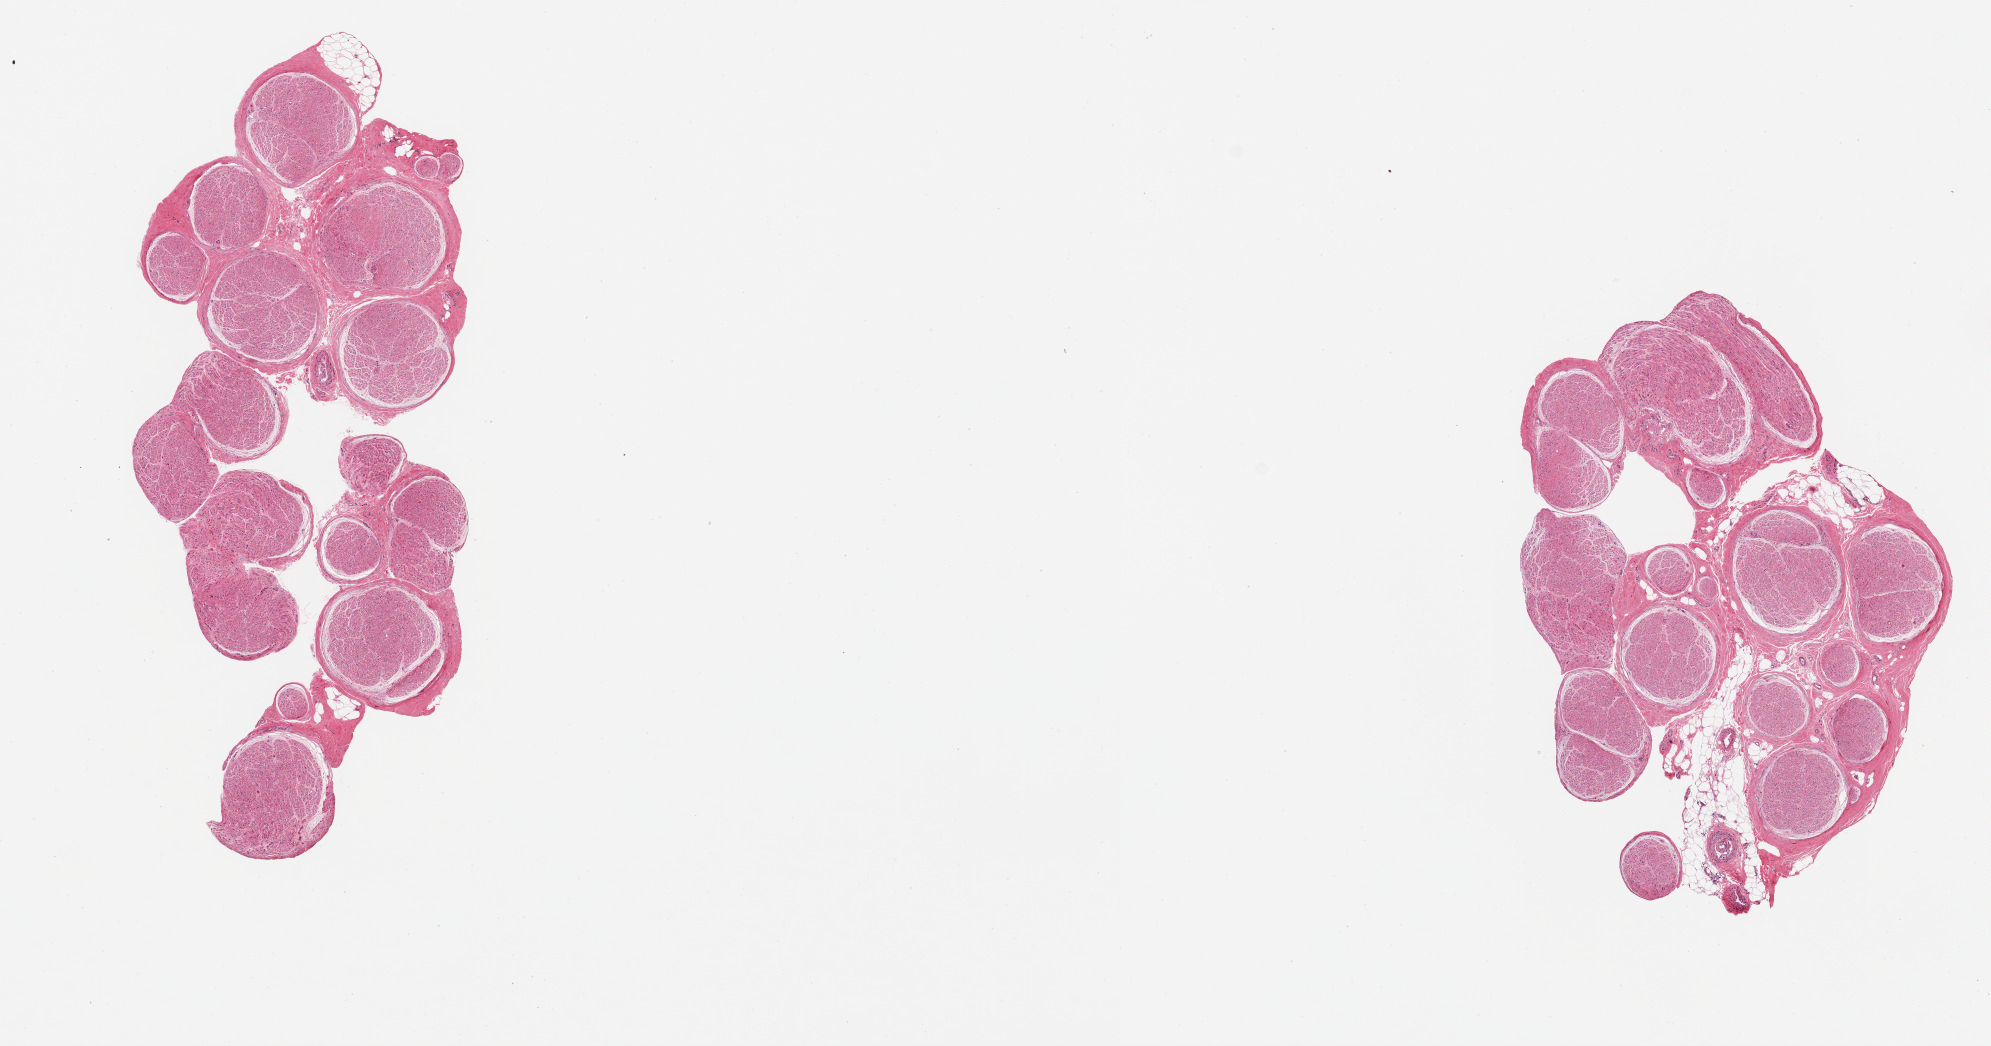
Haematoxylin and eosin whole-slide image, brightfield, shown as a low-resolution overview of the whole scanned area (about 15.8 x 8.3 mm, acquisition: 20x scan); PAXgene-fixed, paraffin-embedded tissue; target tissue: tibial nerve; donor tissue sample. Donor: male.
* pathologist's review note for this sample: 2 pieces; less than 10% internal fat